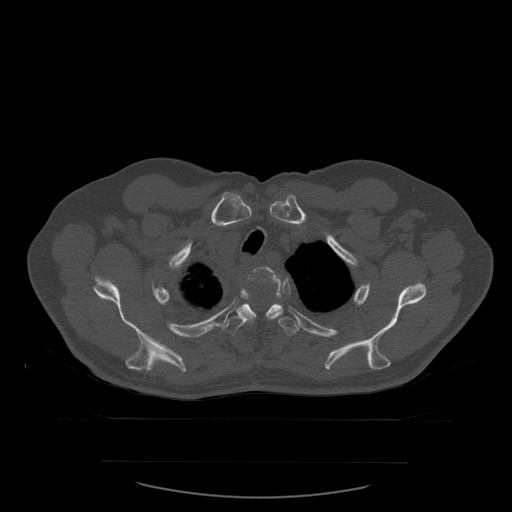
CT including the spine, one axial slice; position 453 of 590 along the scan axis; bone window (W 1800 / L 400 HU); 512 × 512 image matrix, field of view 479 × 479 mm. Patient age 71 years. Case-level facts recorded for this patient, not image findings: primary cancer: lung; vertebrae with lytic lesions (as recorded): T1, T2, L5, S1.
Annotated regions visible in this slice (semi-automatically segmented with operator editing):
- T2 vertebra: bounding box <254,267,281,280> (left, top, right, bottom; pixels)
- T3 vertebra: <237,275,283,320>
- T4 vertebra: <222,295,300,336>